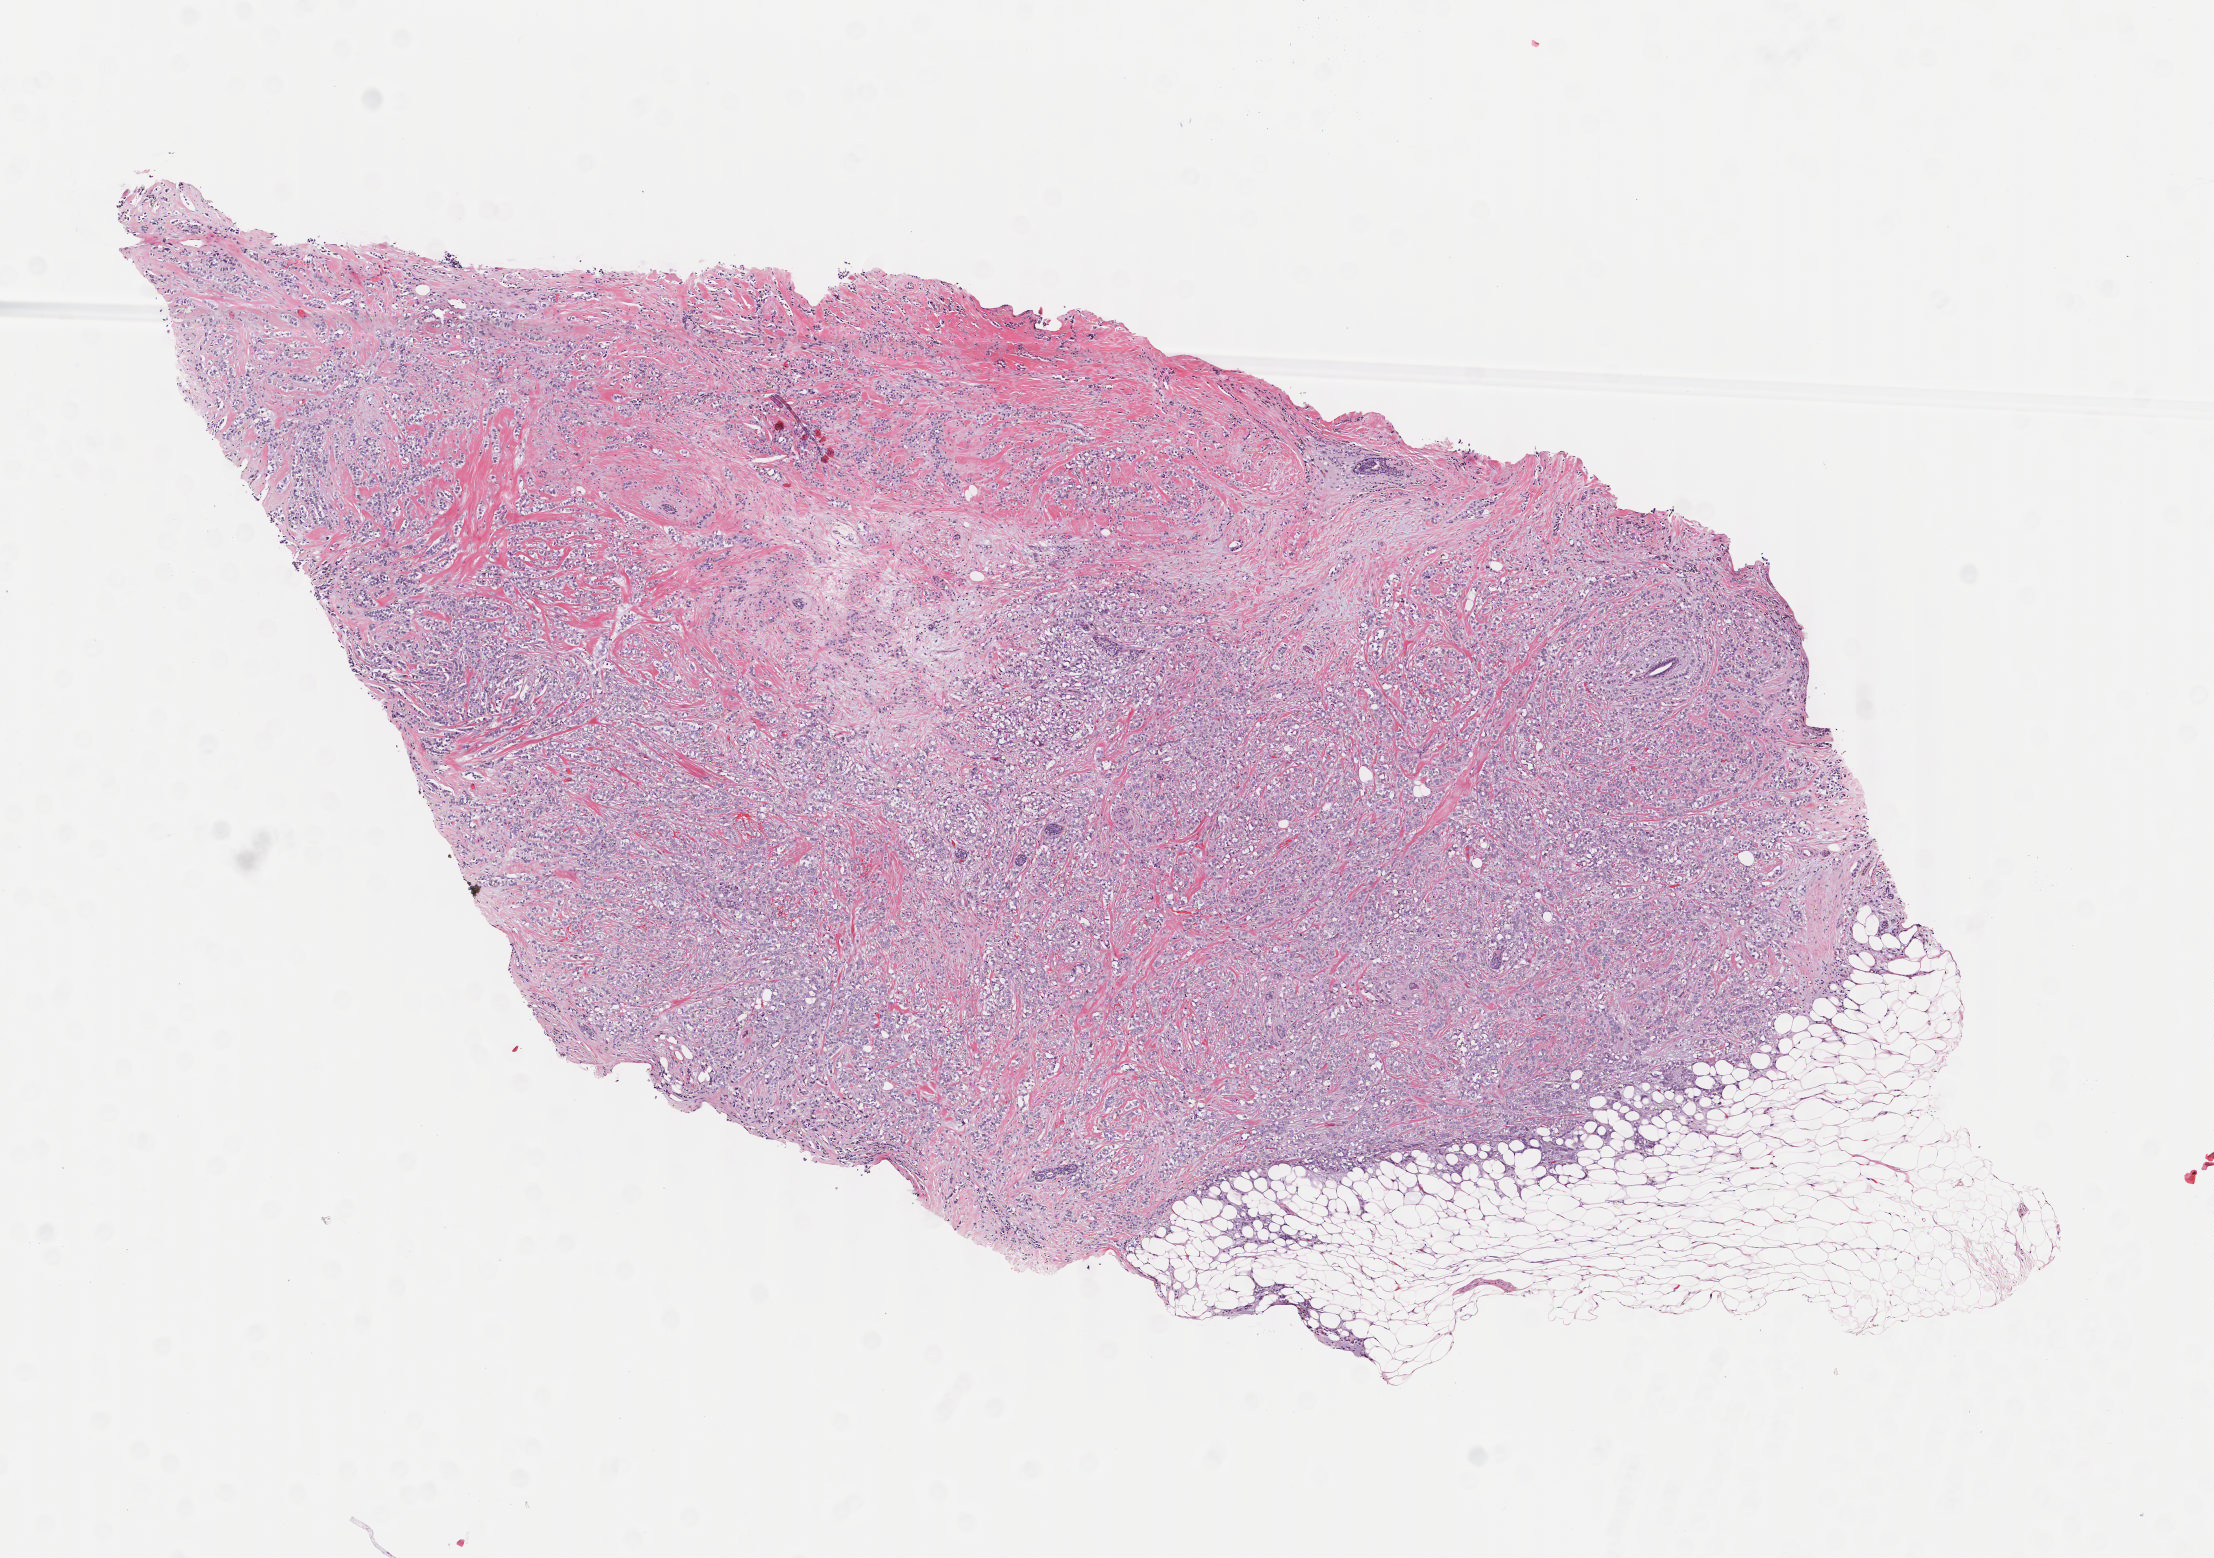
Whole-slide histology image, H&E-stained — whole scanned area (about 8.8 x 6.2 mm, from a 40x scan) shown as a low-resolution overview. Frozen section. Breast, primary tumour sample. Female patient; age at initial diagnosis 71 years. Slide review estimates, as recorded: tumour cells 80%, tumour nuclei 80%, normal cells 0%, stromal cells 20%, necrosis 0%. Infiltration values recorded for this section: lymphocyte infiltration 40%, monocyte infiltration 20%, neutrophil infiltration 20%.
- lymph nodes positive (case pathology): 0 of 16 examined
- histologic diagnosis: Lobular carcinoma, NOS
- AJCC pathologic stage: IIIA